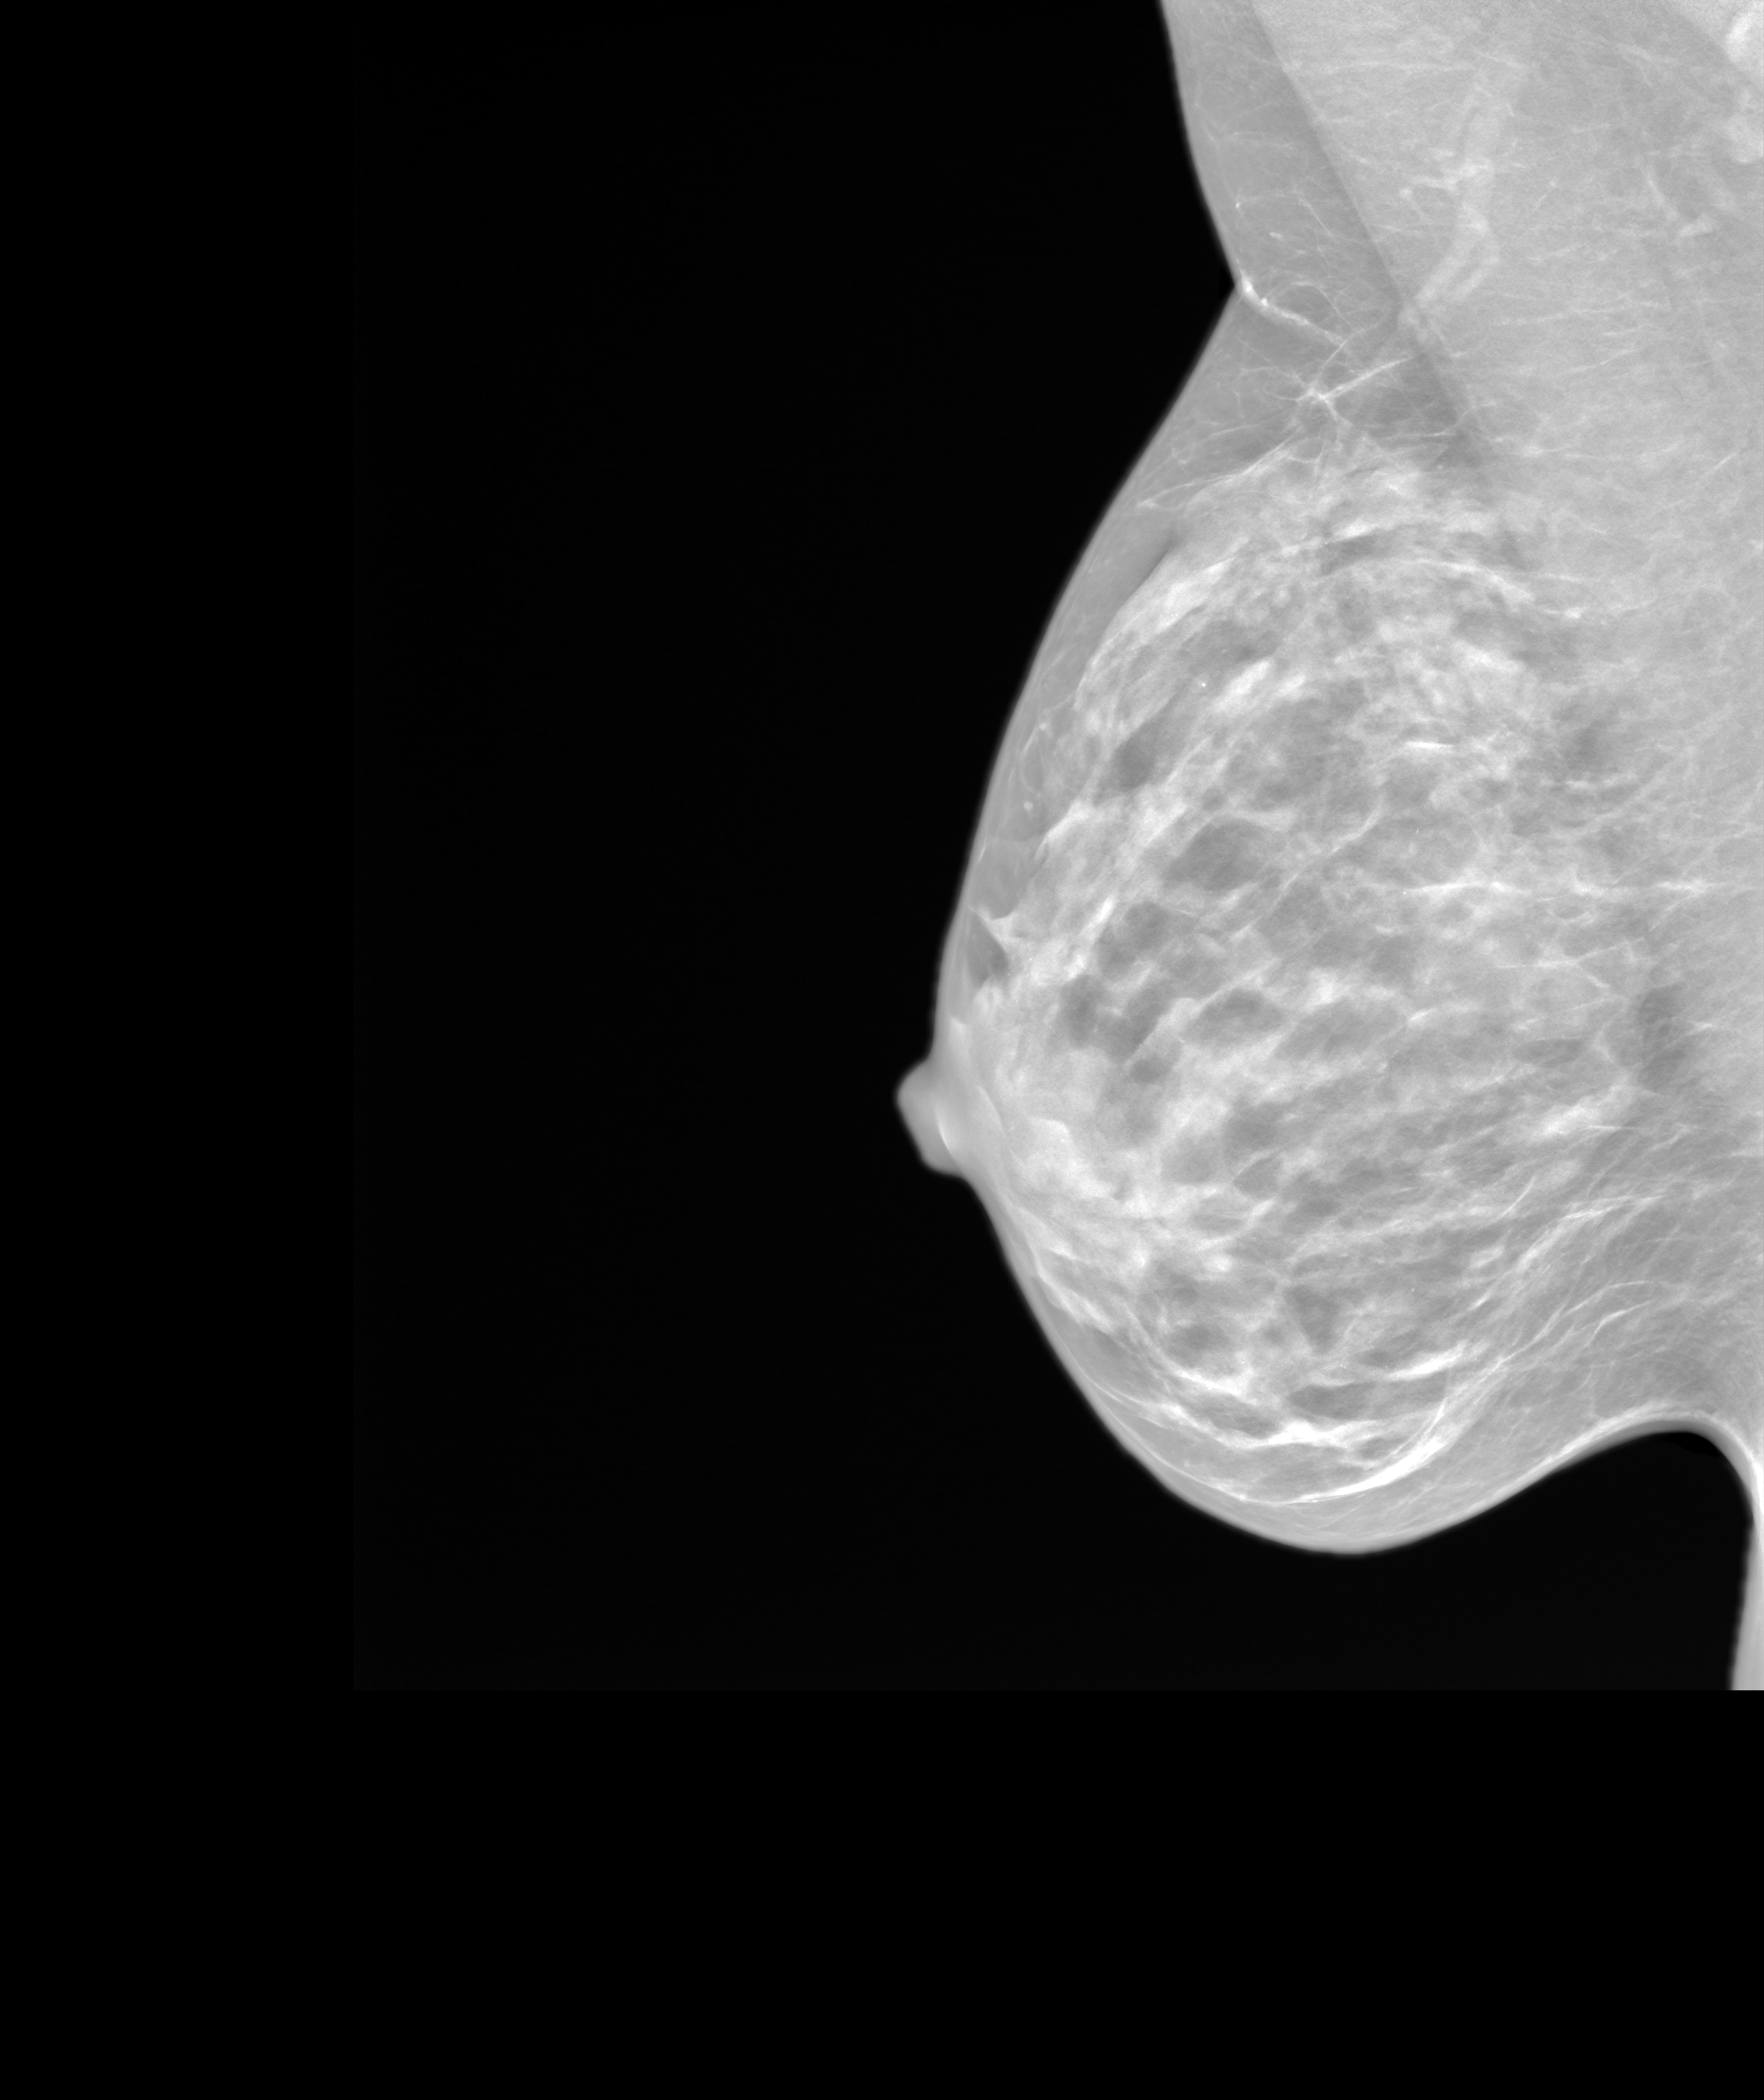
Synthetic 2-D view generated from a tomosynthesis acquisition (not an FFDM exposure); right breast; mediolateral oblique (MLO) view; screening examination; system: SenoIris_1SP1.1(421). Female patient, age 47 years.
BI-RADS breast density category at the screening exam (both breasts, scale 1–4): 3. Final BI-RADS assessment for this screening round (tomosynthesis exam, both breasts): category 3. Recall: recalled for additional imaging after this screen.